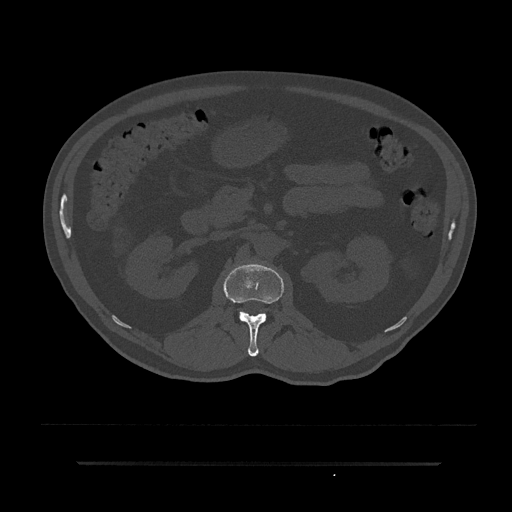
CT including the spine, one axial slice. Slice 126 of 797 in the series (ordered by position). Reconstruction kernel Br40s/3. 120 kVp. Bone window (W 1800 / L 400 HU). 0.5 mm slice thickness. 512 × 512 image matrix, field of view 464 × 464 mm. Patient: male, 59 years. From the clinical record (not read from this slice): primary cancer: bile ducts.
Outlined on this slice (semi-automatically segmented with operator editing):
- L1 vertebra: bounding box [x1, y1, x2, y2] px = [223, 263, 284, 357]